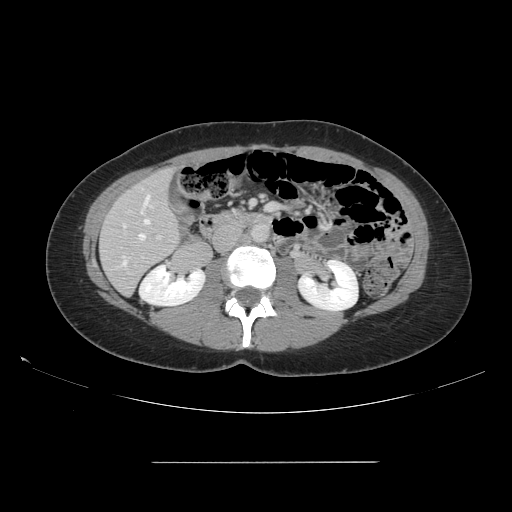
Contrast-enhanced abdominal CT, one axial slice. 120 kVp. Intravenous contrast given. Soft-tissue window (W 400 / L 40 HU). 2.5 mm slice thickness. 512 × 512 image matrix, field of view 421 × 421 mm. Female patient, age 46 years. From the clinical record (not read from this slice): diagnosis: colorectal cancer liver metastases, imaged before liver resection; multiple liver metastases: yes; largest metastasis: 3 cm; disease in both lobes: yes.
Structures marked on this image (outlined manually by an expert reader):
- hepatic veins: bounding box (x1, y1, x2, y2) in pixels: (122, 194, 150, 266)
- liver: (100, 170, 180, 294)
- planned liver remnant (the part of the liver to remain after resection): (100, 170, 179, 294)
- portal vein (with intrahepatic branches): (157, 236, 161, 239)